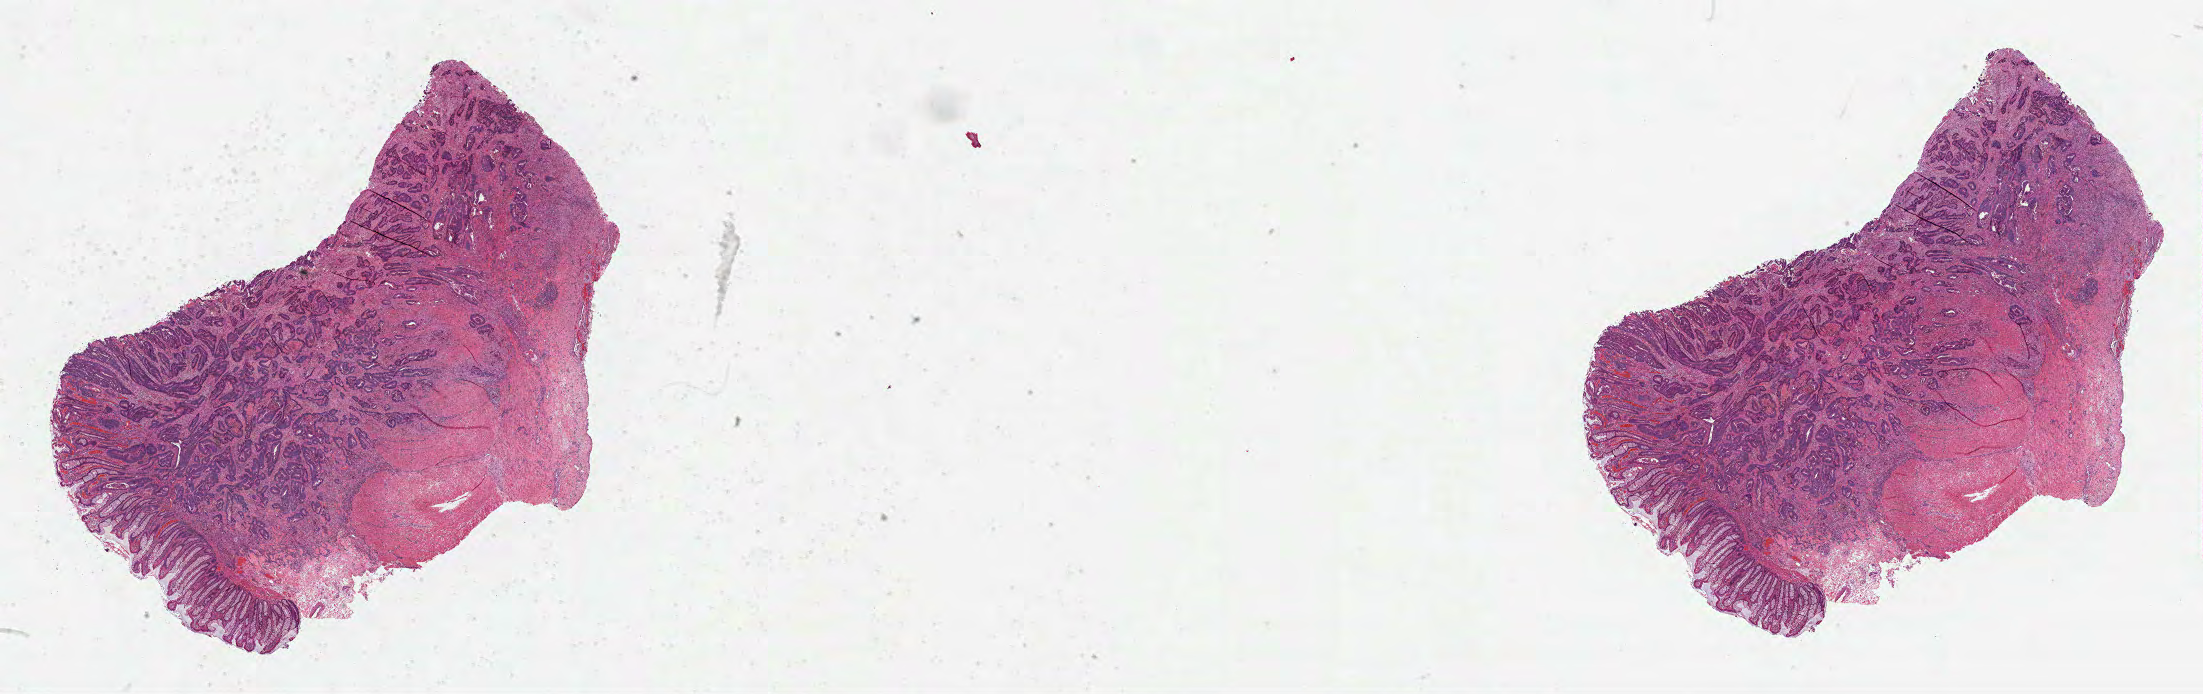
Whole-slide histology image, Hematoxylin and eosin (H&E) stained, shown as a low-resolution overview of the whole scanned area (about 35.5 x 11.2 mm, acquisition: 40x scan); formalin-fixed paraffin-embedded (FFPE) diagnostic section; colon, primary tumour sample. Female patient; age at initial diagnosis 65 years.
AJCC pathologic stage: IIIB (7th edition). Diagnosis: Adenocarcinoma, NOS.